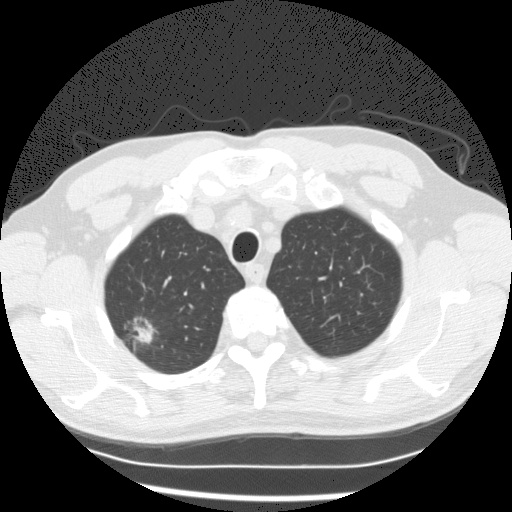
Low-dose screening chest CT, axial slice. First (baseline) screen. Lung window (W 1500 / L -600 HU). Slice 22 of 132 in the series. 512 × 512 image matrix, field of view 351 × 351 mm. Male participant, aged 63 years at enrolment. Current smoker at enrolment.
Expert reader's lesion annotation, bounding box <105,302,171,363> (left, top, right, bottom; pixels). The exam's reader record, not a measurement of the box and not confirmed to be the same lesion: non-calcified nodule or mass ≥4 mm, right upper lobe, 19 × 9 mm, poorly defined margins, mixed attenuation. Official screen result: positive, change unspecified: nodule(s) >= 4 mm or enlarging nodule(s), mass(es), or other non-specific abnormalities suspicious for lung cancer.